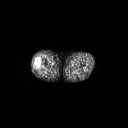
FDG PET of an extremity soft-tissue mass (from a PET/CT study), one axial slice. Slice 230 of 267 in the series (ordered by position). 3.27 mm slice thickness. 128 × 128 image matrix, field of view 700 × 700 mm. Male patient, age 43 years. Case-level facts recorded for this patient, not image findings: histological type: poorly differentiated synovial sarcoma; grade: high; site of the primary tumour: right buttock.
Outlined on this slice (expert contour drawn on MRI and transferred to this co-registered scan by the dataset authors):
- gross tumour volume including surrounding oedema: box from (x=34, y=59) to (x=44, y=69) px
- gross tumour volume (mass): (x=34, y=59)–(x=41, y=68)